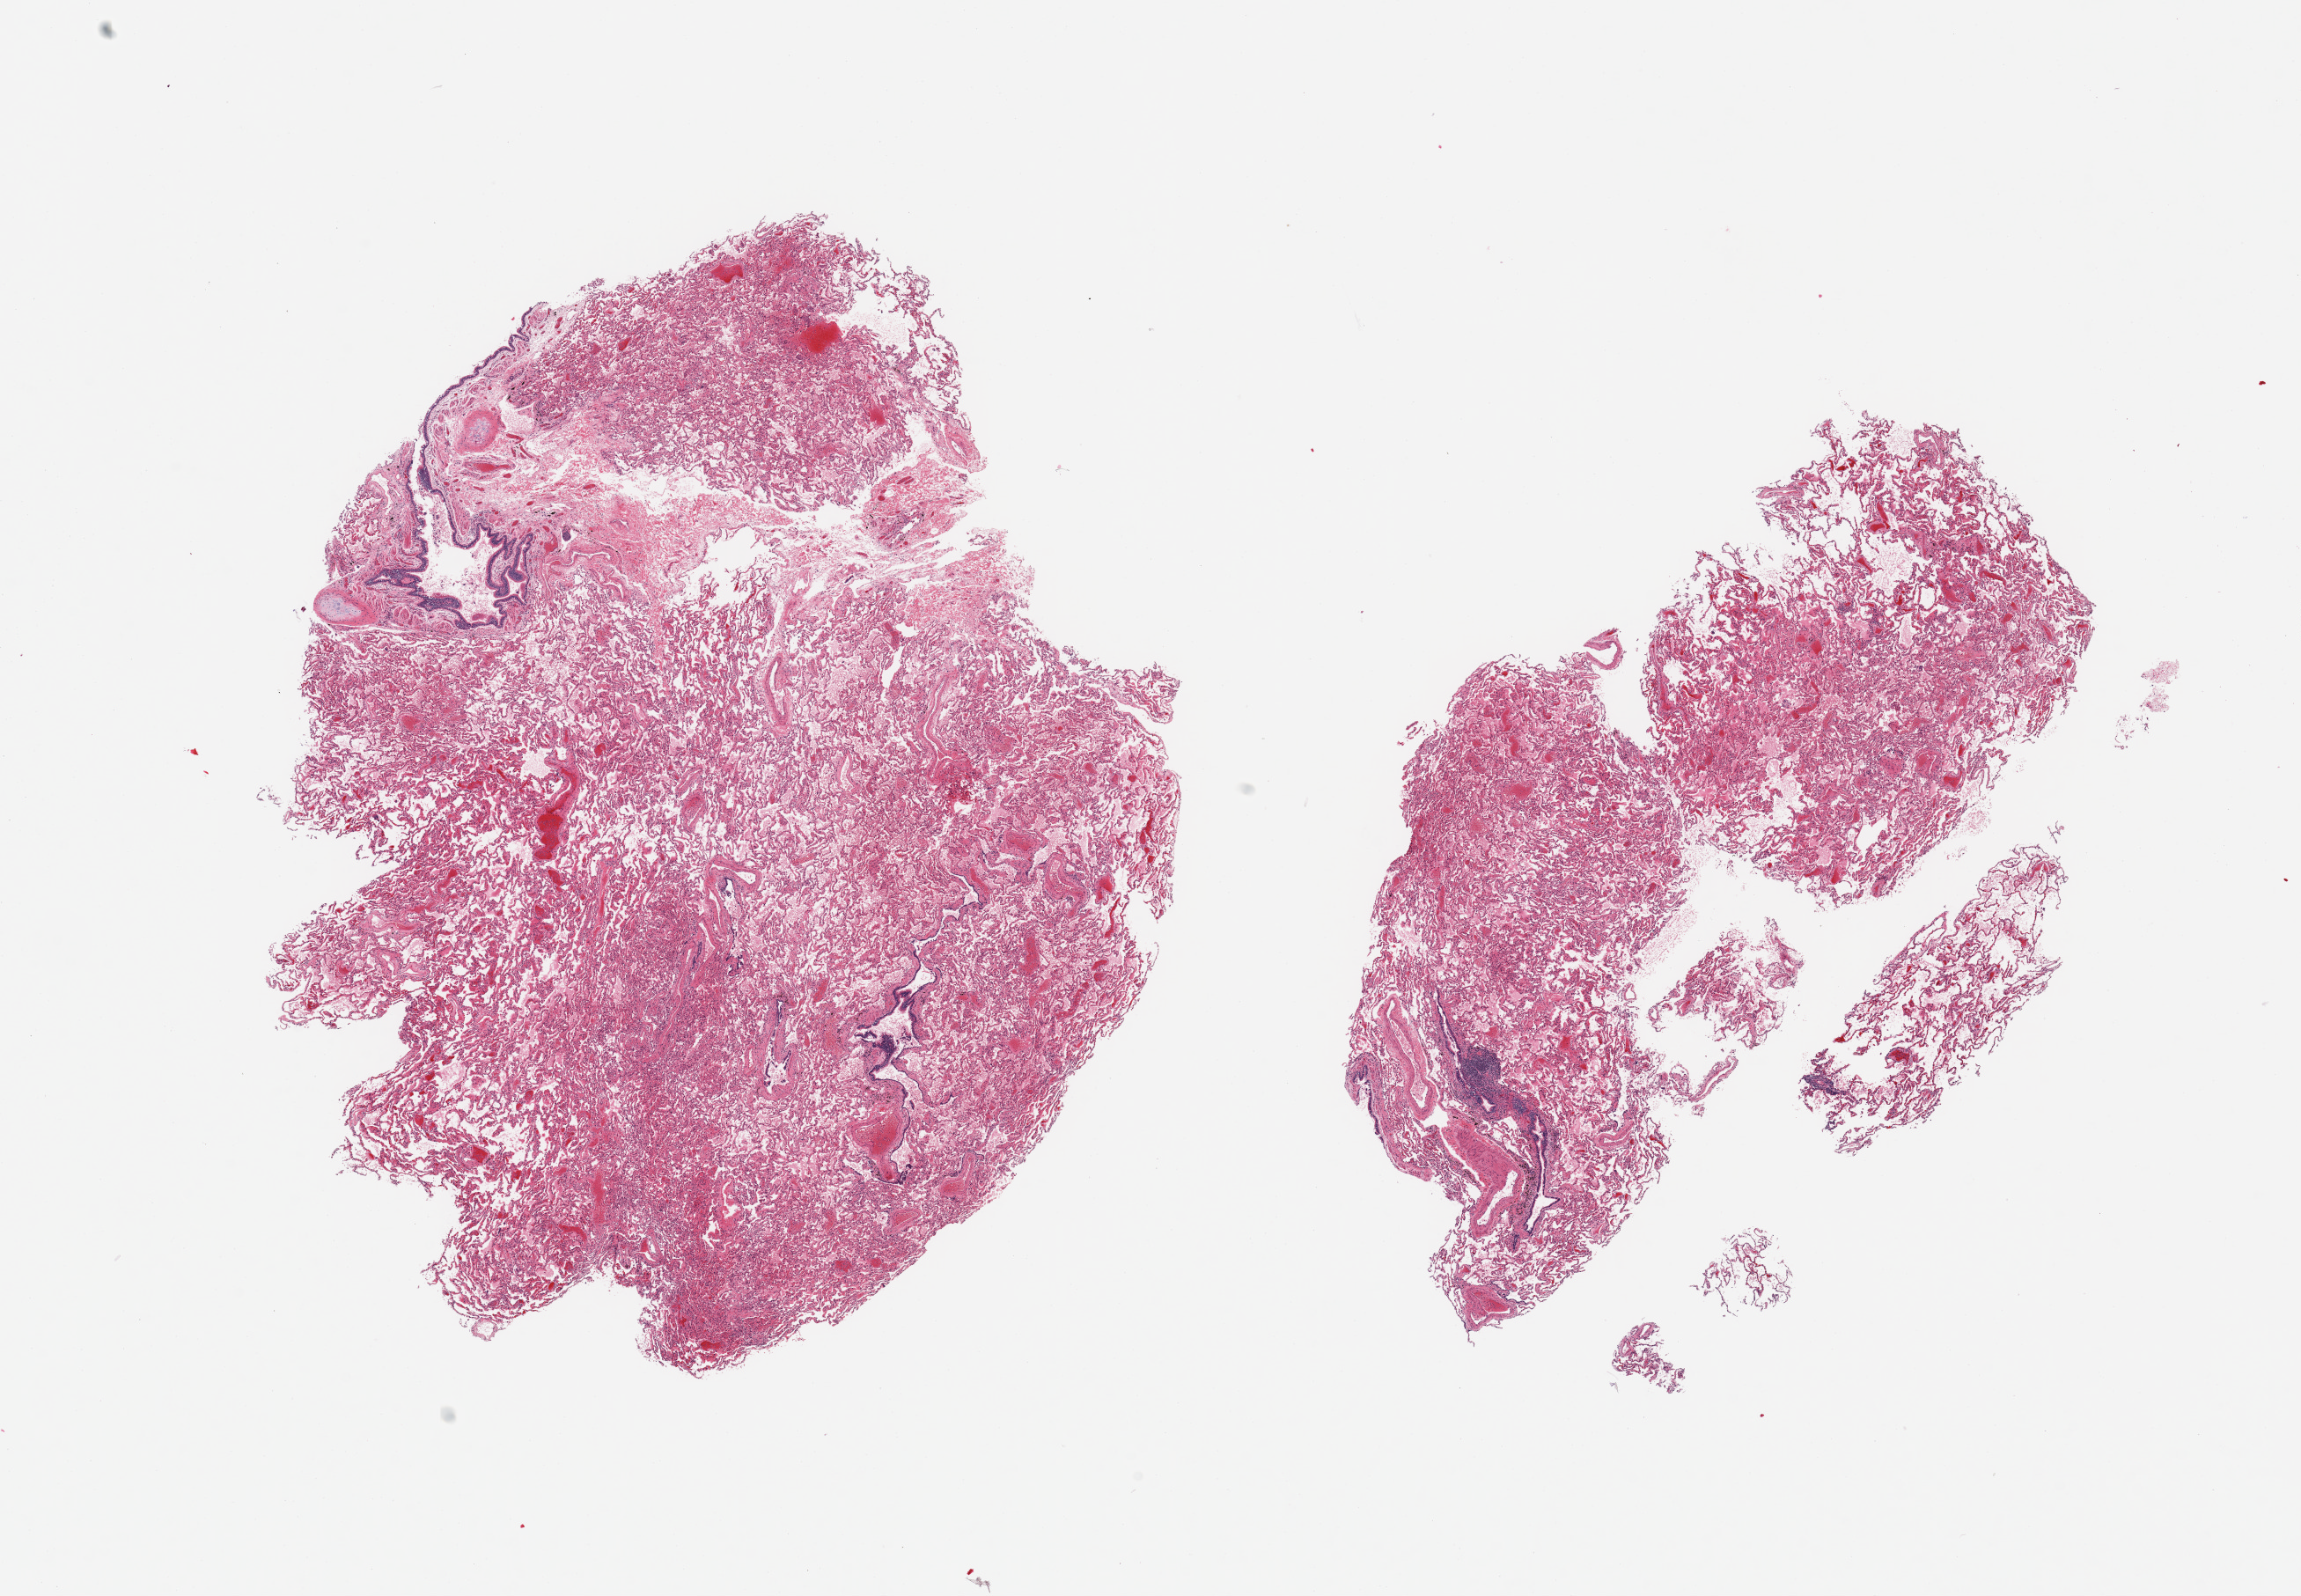
H&E whole-slide image — shown as a low-resolution overview of the whole scanned area (about 20.7 x 14.3 mm). PAXgene-fixed paraffin-embedded (PFPE) section. Target tissue: lung. Tissue donor sample.
Review note (as recorded): 2 pieces; moderate pulmonary edema and congestion; scattered foci of pigmented alveolar macrophages.